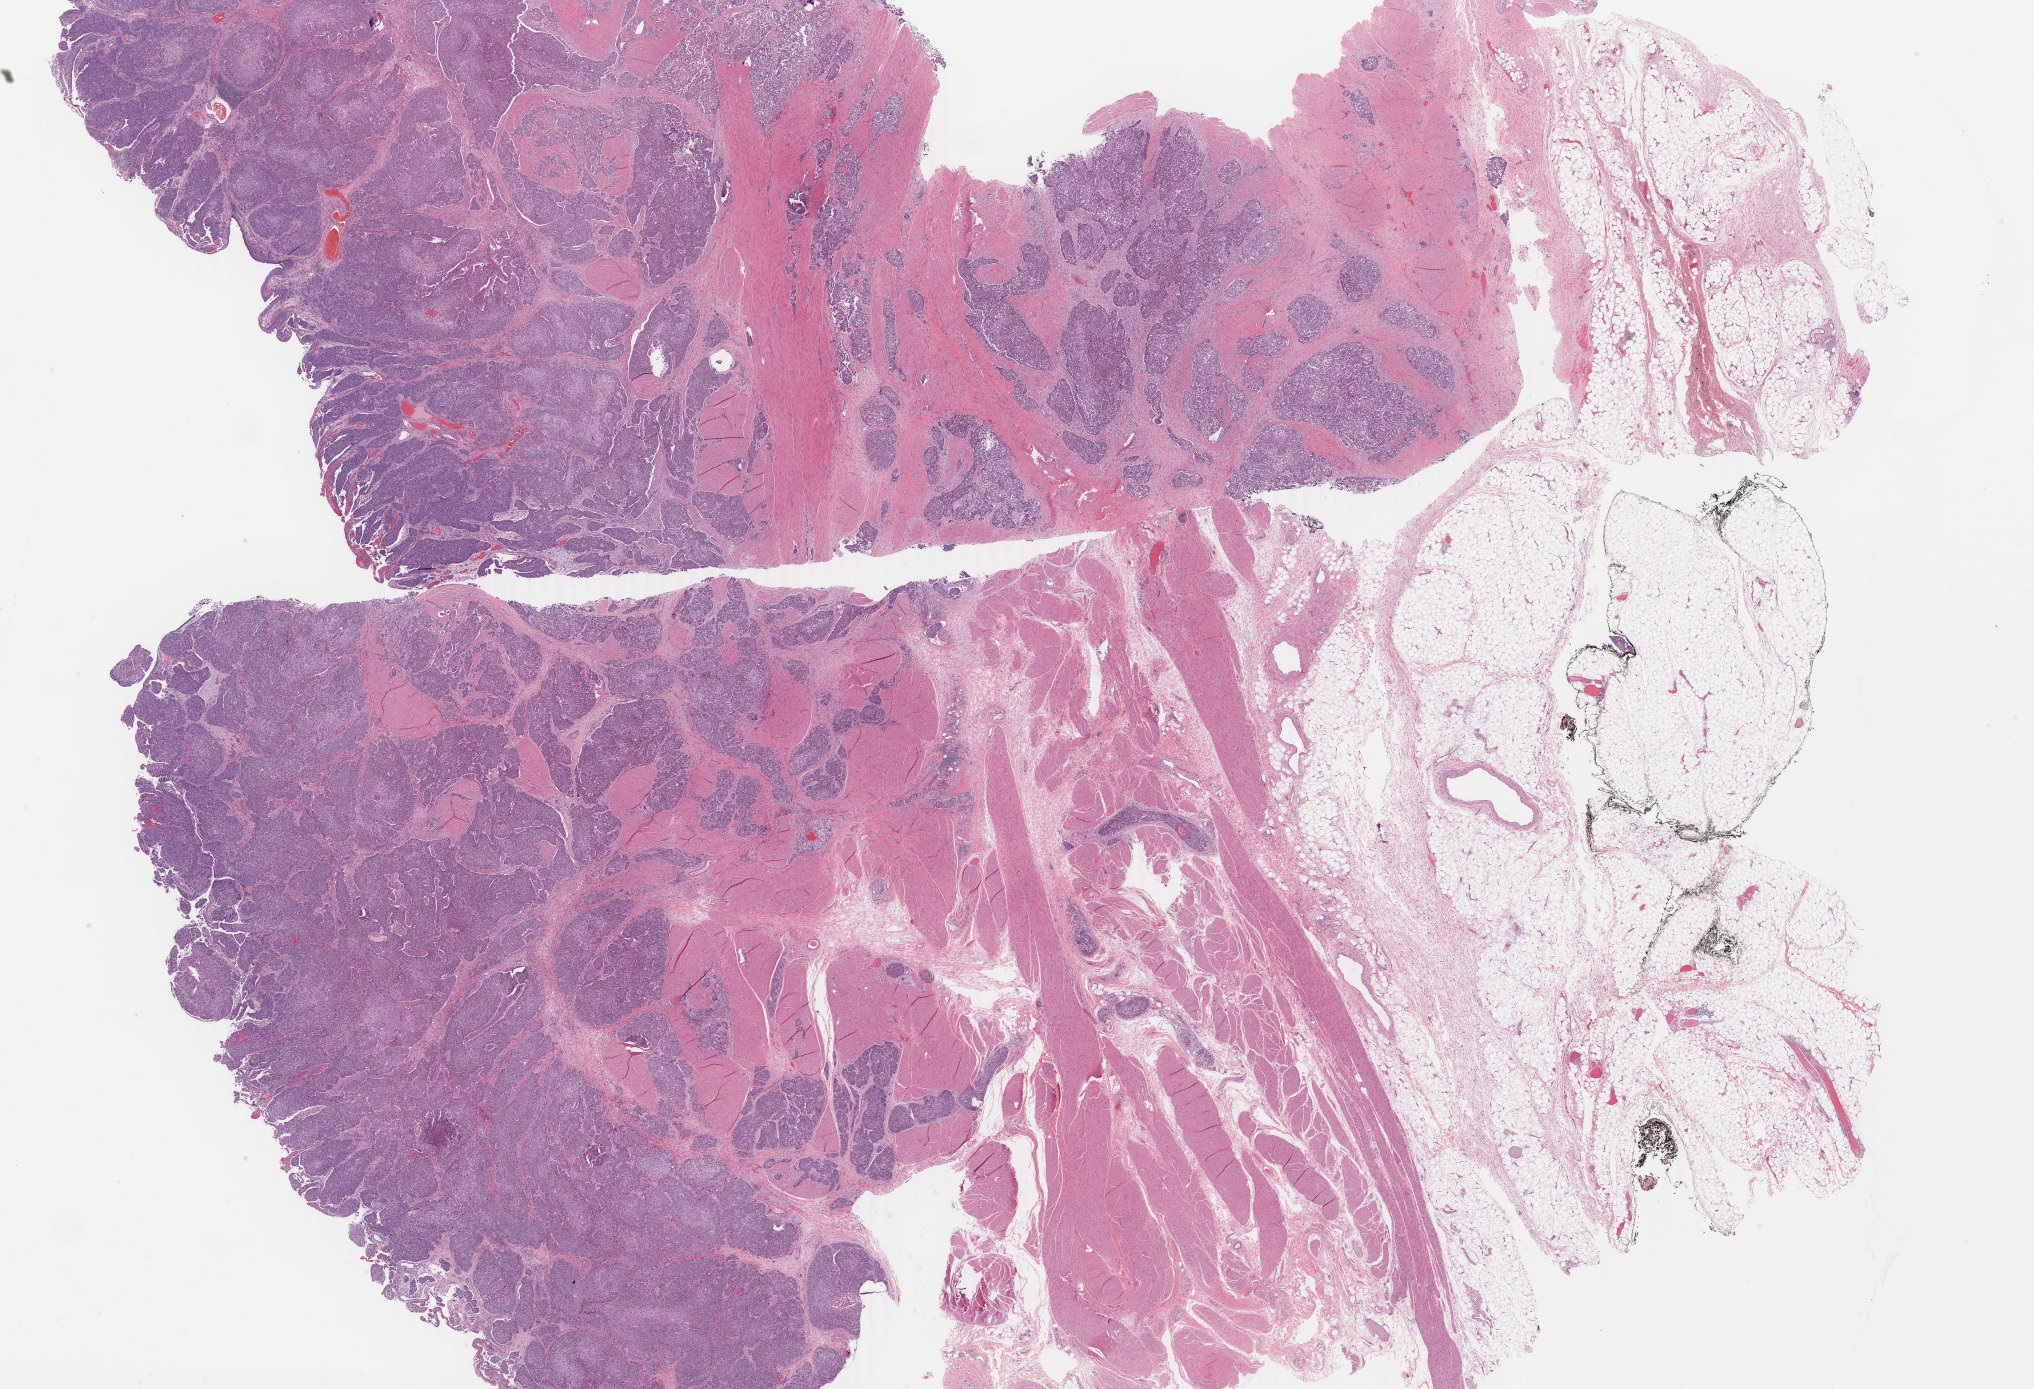
Hematoxylin and eosin (H&E) stained whole-slide image, shown as a low-resolution overview of the whole scanned area (about 32.4 x 22.1 mm, from a 40x scan), formalin-fixed paraffin-embedded (FFPE) diagnostic section, bladder, primary tumour sample. Patient: male, age at initial diagnosis 70 years. Histologic grade: high grade.
* lymph nodes positive (case pathology): 4 of 25 examined
* AJCC pathologic stage: IV (7th edition)
* pathologic diagnosis: Transitional cell carcinoma (lateral wall of bladder)